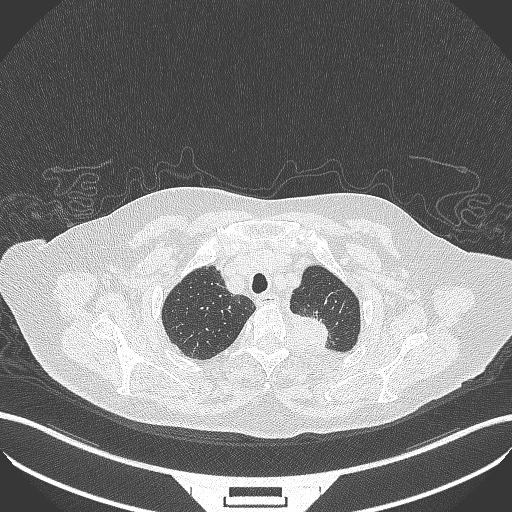
Chest CT, one axial slice; slice 300 of 353 in the series (ordered by position); reconstruction kernel B70f; 100 kVp; lung window (W 1500 / L -600 HU); 1 mm slice thickness; 512 × 512 image matrix, field of view 400 × 400 mm. Female patient, age 81 years. From the clinical record (not read from this slice): clinical TNM (as recorded): T2a N0 M0.
Outlined on this slice (bounding box drawn by a radiologist):
- lung tumour (recorded histology: adenocarcinoma): bounding box <287,309,338,348> (left, top, right, bottom; pixels)